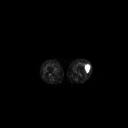
FDG PET of an extremity soft-tissue mass (from a PET/CT study), one axial slice; slice 171 of 223 in the series (ordered by position); 128 × 128 image matrix, field of view 700 × 700 mm. Patient: female, 16 years. Case-level facts recorded for this patient, not image findings: histological type: spindle cell suggestive of biphasic synovial sarcoma; grade: intermediate; site of the primary tumour: left knee.
Outlined on this slice (expert contour drawn on MRI and transferred to this co-registered scan by the dataset authors):
- gross tumour volume including surrounding oedema: bounding box <85,63,90,72> (left, top, right, bottom; pixels)
- gross tumour volume (mass): <85,63,90,72>